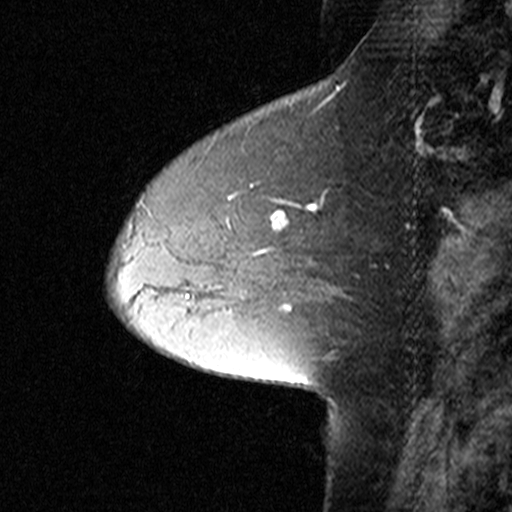
Breast MRI (dynamic contrast-enhanced), one sagittal slice. Slice 14 of 44 in the series (ordered by position). Dynamic contrast-enhanced study with each time point stored as its own series, time point 2 of 3 at this slice position (early post-contrast, ordered by acquisition time). 1.5 T. TE 4.5 ms, TR 11 ms. 3 mm slice thickness. 512 × 512 image matrix, field of view 200 × 200 mm. Patient: female, 50 years. From the clinical record (not read from this slice): setting: breast cancer imaged before/during neoadjuvant chemotherapy; receptor status: HR-positive, HER2-negative.
Outlined on this slice (semi-automatically segmented with operator editing):
- analysis volume of interest (the breast-tissue region the enhancement analysis was run in; not a lesion): bounding box <126,162,292,291> (left, top, right, bottom; pixels)
- tumour enhancement mask (voxels above the 90 % enhancement threshold inside the analysis volume of interest): <136,185,288,254>